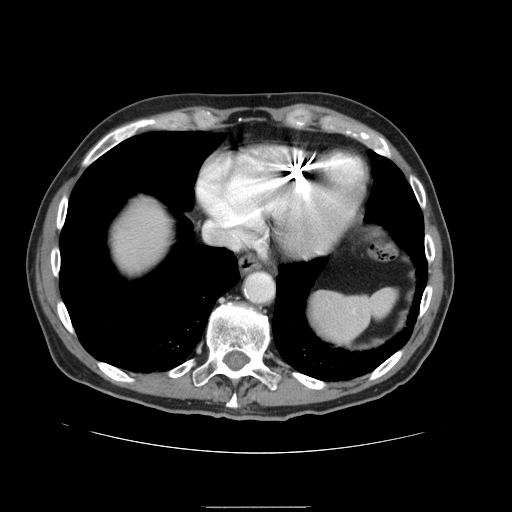
Contrast-enhanced abdominal CT, one axial slice. Slice 137 of 168 in the series (ordered by position). 120 kVp. Intravenous contrast given. Soft-tissue window (W 400 / L 40 HU). 2.5 mm slice thickness. 512 × 512 image matrix. Male patient, age 74 years. From the clinical record (not read from this slice): diagnosis: colorectal cancer liver metastases, imaged before liver resection; multiple liver metastases: no; largest metastasis: 14.5 cm; disease in both lobes: yes.
Outlined on this slice (expert manual segmentation):
- liver: bounding box (x1, y1, x2, y2) in pixels: (106, 196, 174, 278)
- planned liver remnant (the part of the liver to remain after resection): (106, 195, 174, 278)